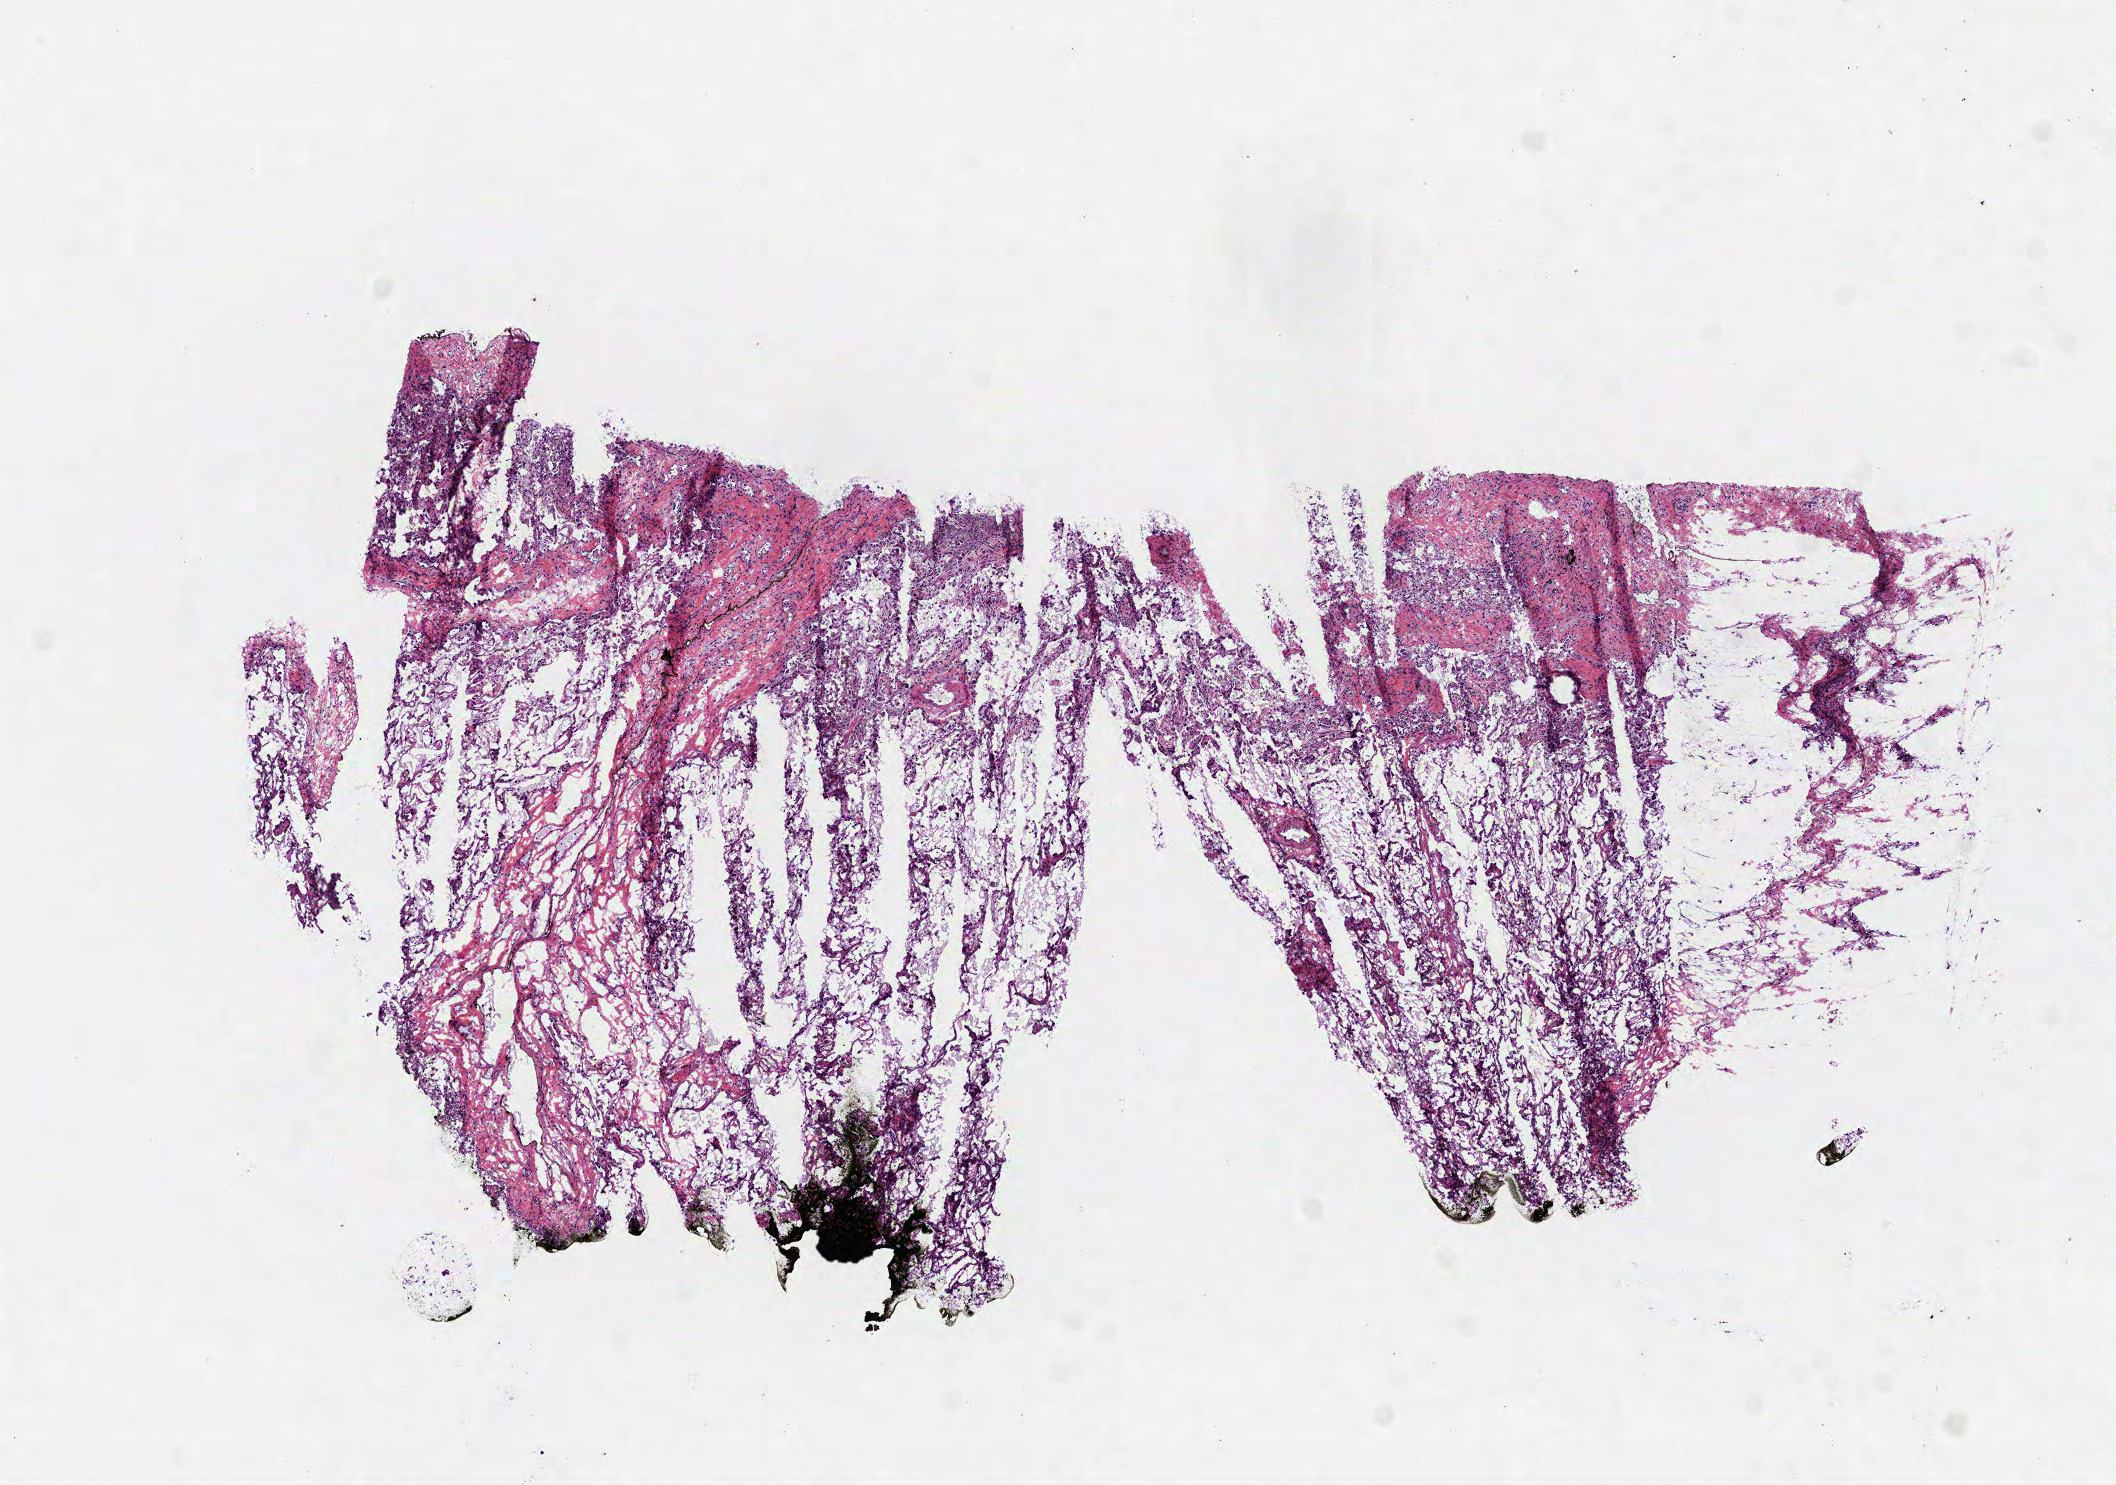
Digitized H&E tissue section (whole slide), shown as a low-resolution overview of the whole scanned area (about 8.5 x 6.0 mm, acquisition: 40x scan). Frozen section from the top of the tissue portion. Lung, solid tissue normal (non-tumour tissue) sample. Male patient; age at initial diagnosis 68 years.
This section: solid tissue normal sample (biorepository sample class). Patient diagnosis: Squamous cell carcinoma, NOS.